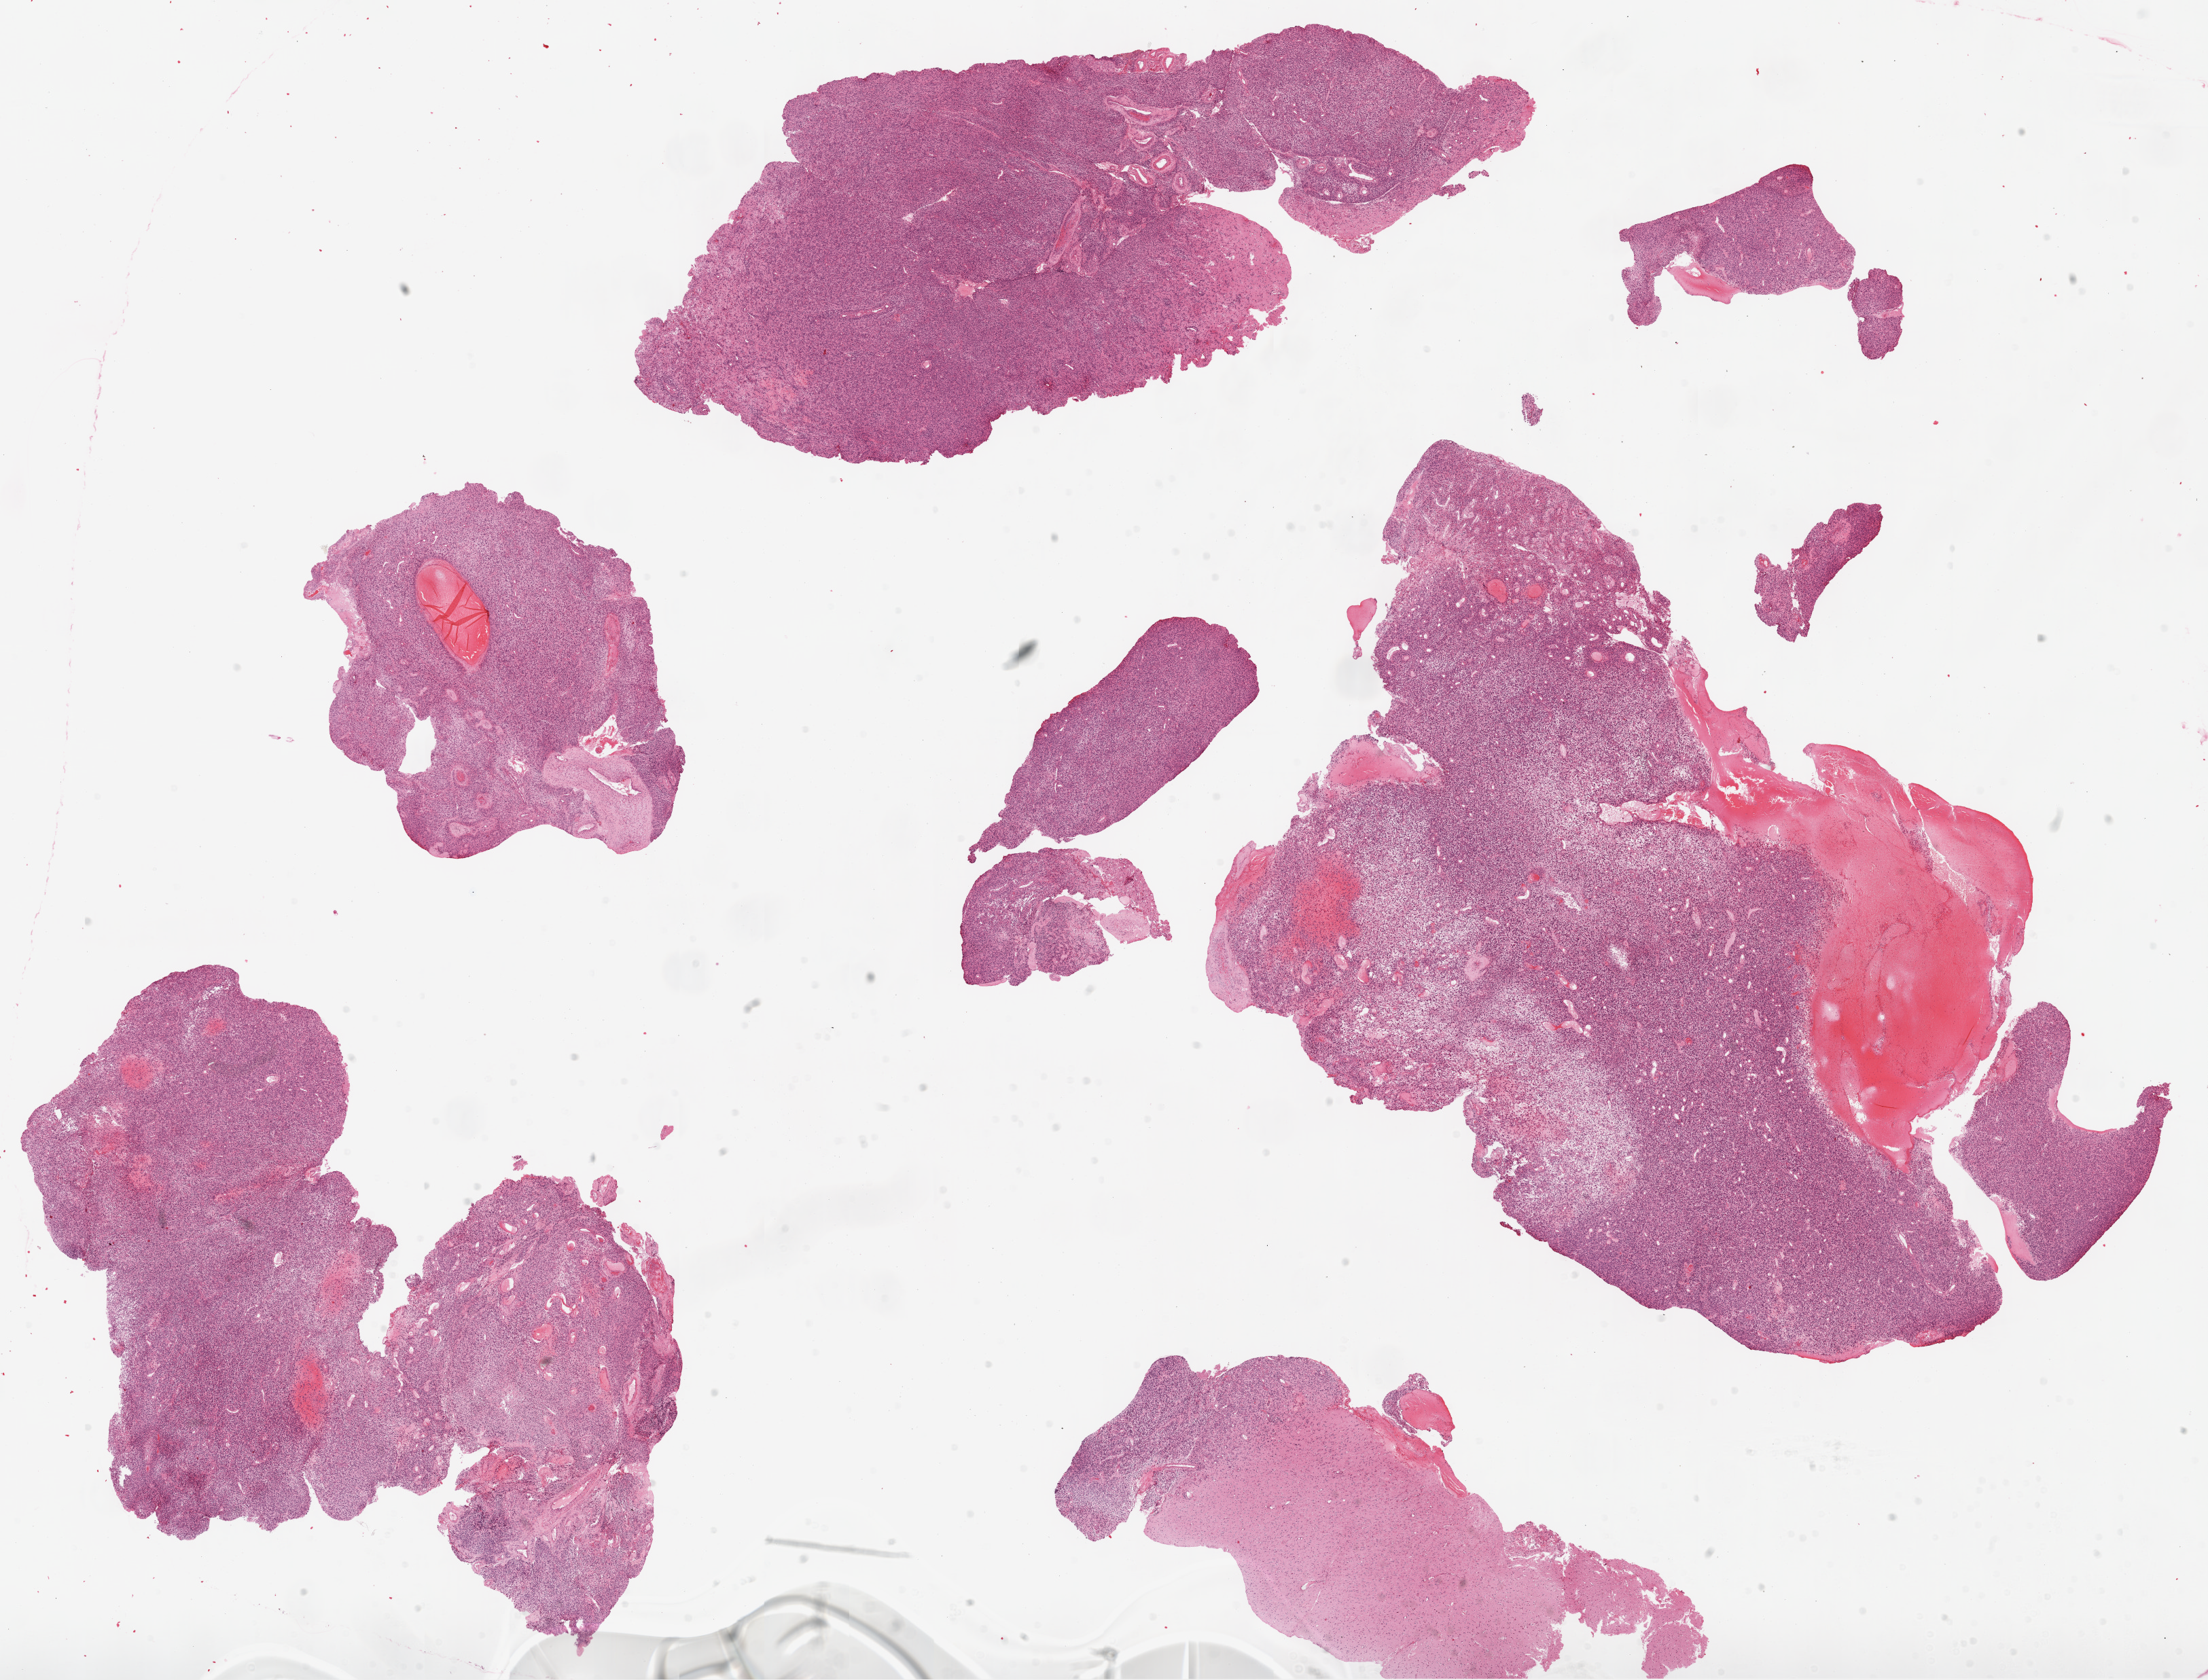
Whole-slide histology image, H&E — low-resolution overview of the scanned area, about 26.1 x 19.8 mm, FFPE section, brain, primary tumour sample. Female, age 67 years at initial diagnosis.
Histologic diagnosis: Glioblastoma.